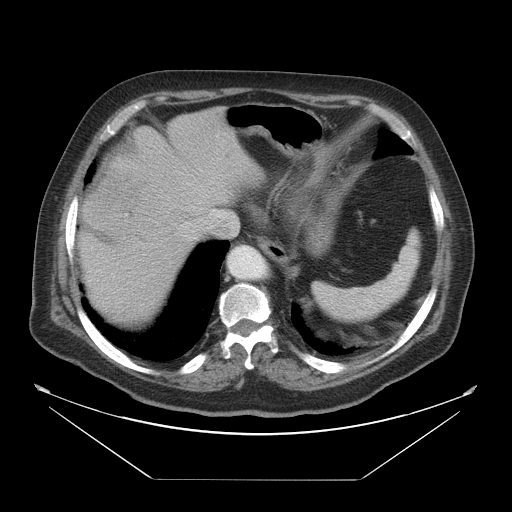
Contrast-enhanced abdominal CT, one axial slice. Position 41 of 45 along the scan axis. Reconstruction kernel STANDARD. Intravenous contrast given. Soft-tissue window (W 400 / L 40 HU). 512 × 512 image matrix, field of view 463 × 463 mm. Male patient, age 87 years. Case-level facts recorded for this patient, not image findings: diagnosis: colorectal cancer liver metastases, imaged before liver resection; multiple liver metastases: no; largest metastasis: 4.5 cm; chemotherapy before resection: no.
Structures marked on this image (outlined manually by an expert reader):
- hepatic veins: bounding box [x1, y1, x2, y2] px = [182, 207, 202, 229]
- liver: [80, 108, 265, 328]
- planned liver remnant (the part of the liver to remain after resection): [116, 108, 265, 209]
- liver metastasis: [123, 230, 152, 250]
- liver metastasis: [94, 166, 152, 215]